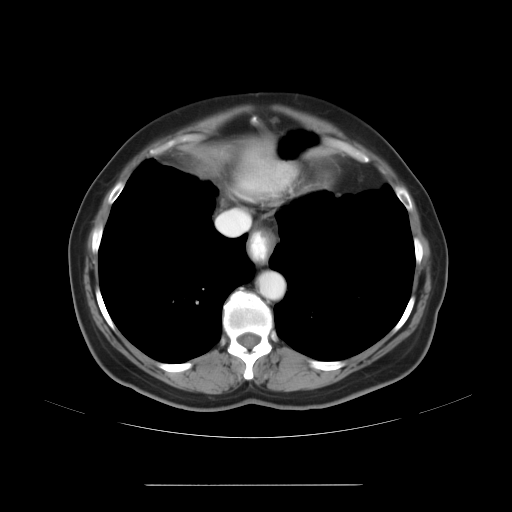
Contrast-enhanced abdominal CT, one axial slice; position 26 of 27 along the scan axis; 120 kVp; intravenous contrast given; soft-tissue window (W 400 / L 40 HU); 512 × 512 image matrix, field of view 440 × 440 mm. Female patient, age 58 years. From the clinical record (not read from this slice): diagnosis: colorectal cancer liver metastases, imaged before liver resection; multiple liver metastases: yes; largest metastasis: 1.9 cm; disease in both lobes: yes.
Annotated regions visible in this slice (expert manual segmentation):
- liver: bounding box (x1, y1, x2, y2) in pixels: (235, 169, 272, 188)
- planned liver remnant (the part of the liver to remain after resection): (235, 169, 272, 188)